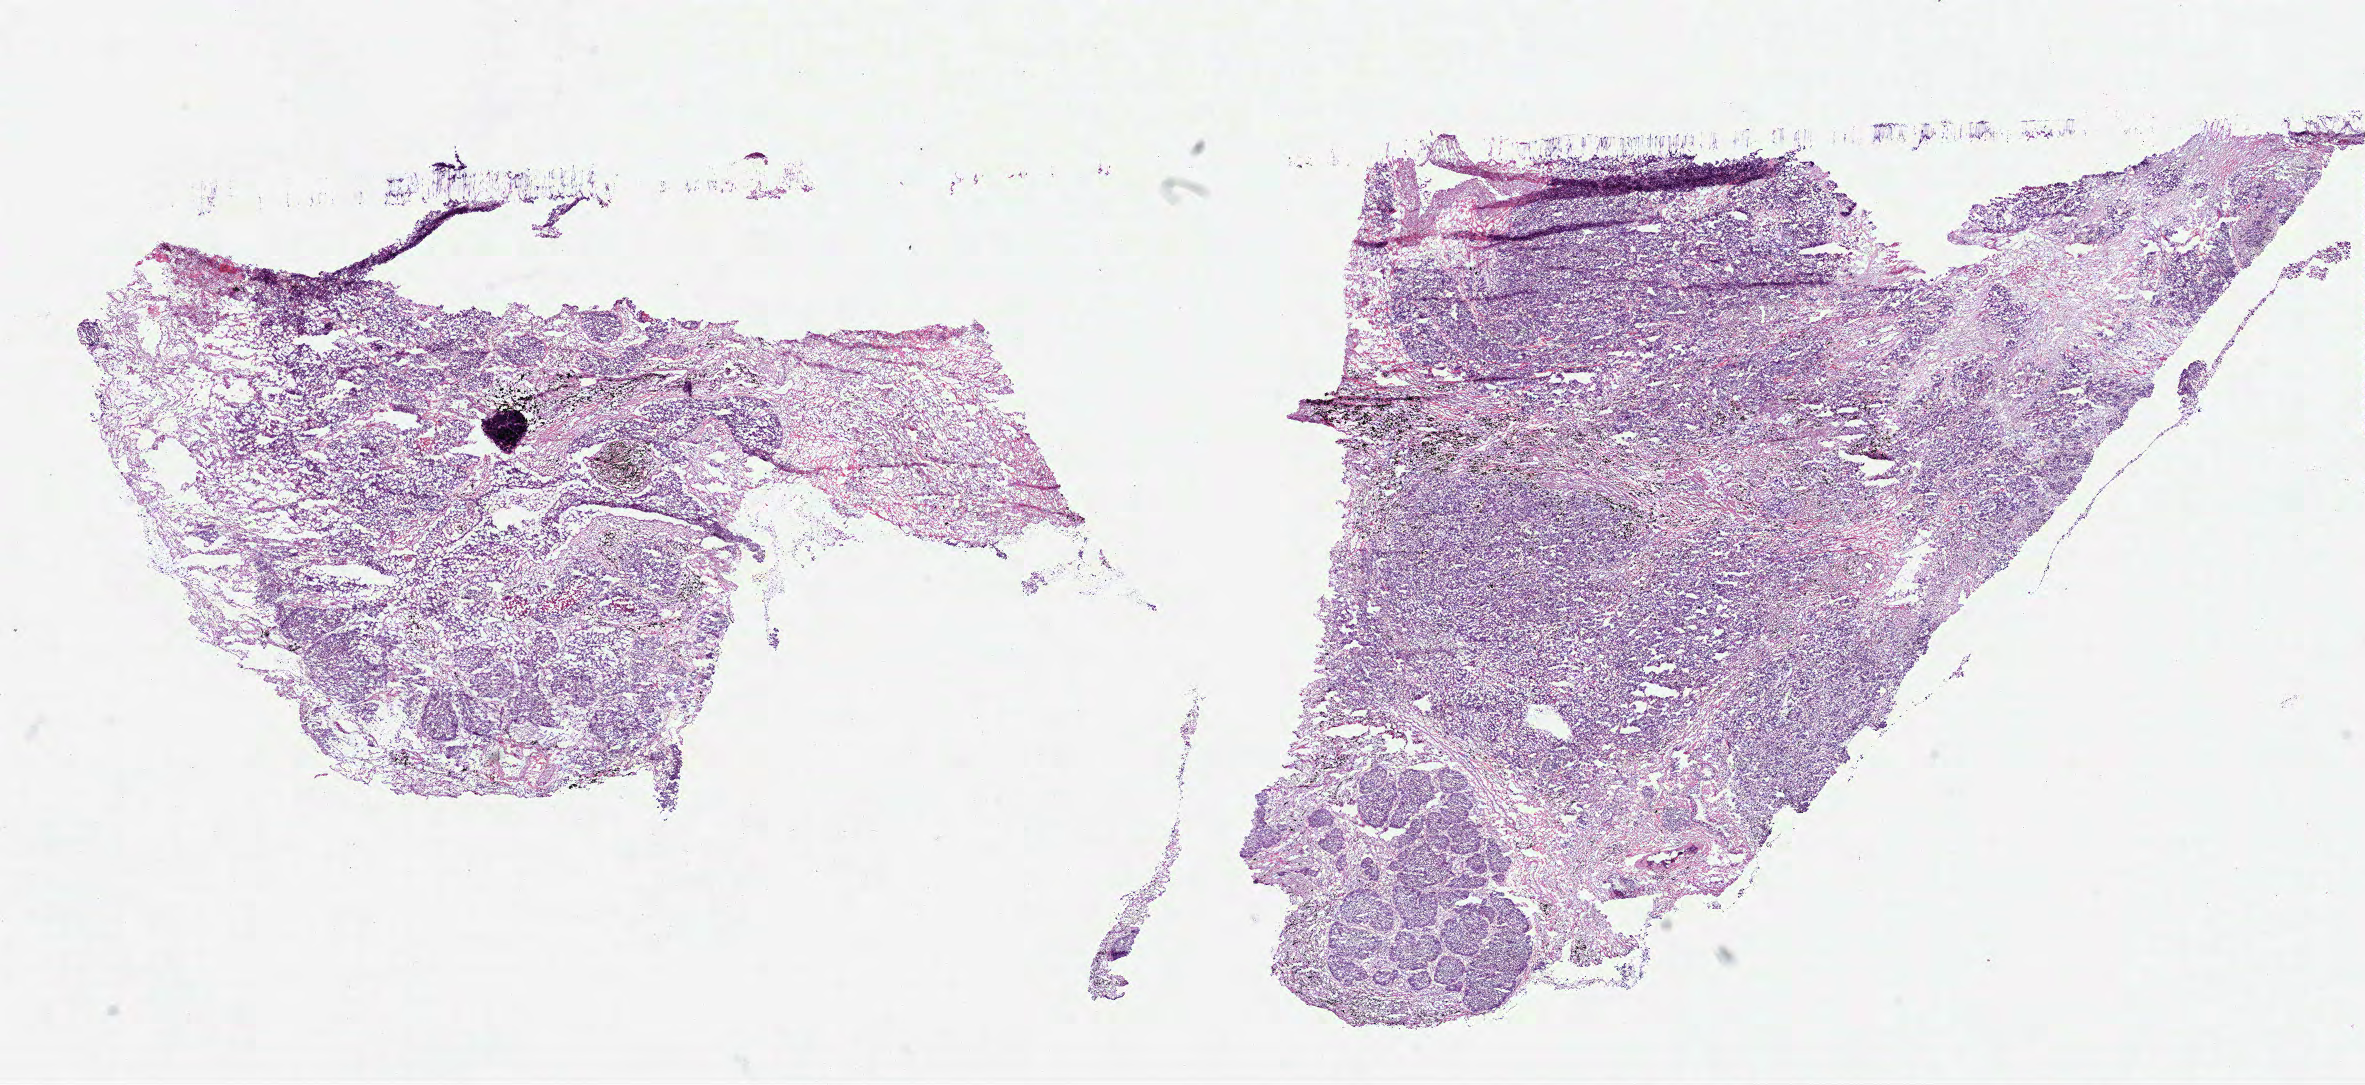
Whole-slide histology image, H&E-stained, shown as a low-resolution overview of the whole scanned area (about 19.1 x 8.8 mm), frozen section from the bottom of the tissue portion, sample: primary tumour, lung. Female, age 75 years at initial diagnosis. Composition of this section per pathologist review: tumour cells 85%, tumour nuclei 80%, normal cells 0%, stromal cells 10%, necrosis 5%. Inflammatory infiltration, as recorded: lymphocyte infiltration 10%, monocyte infiltration 2%, neutrophil infiltration 5%.
AJCC pathologic stage: IB. Pathologic diagnosis: Adenocarcinoma, NOS (upper lobe, lung).